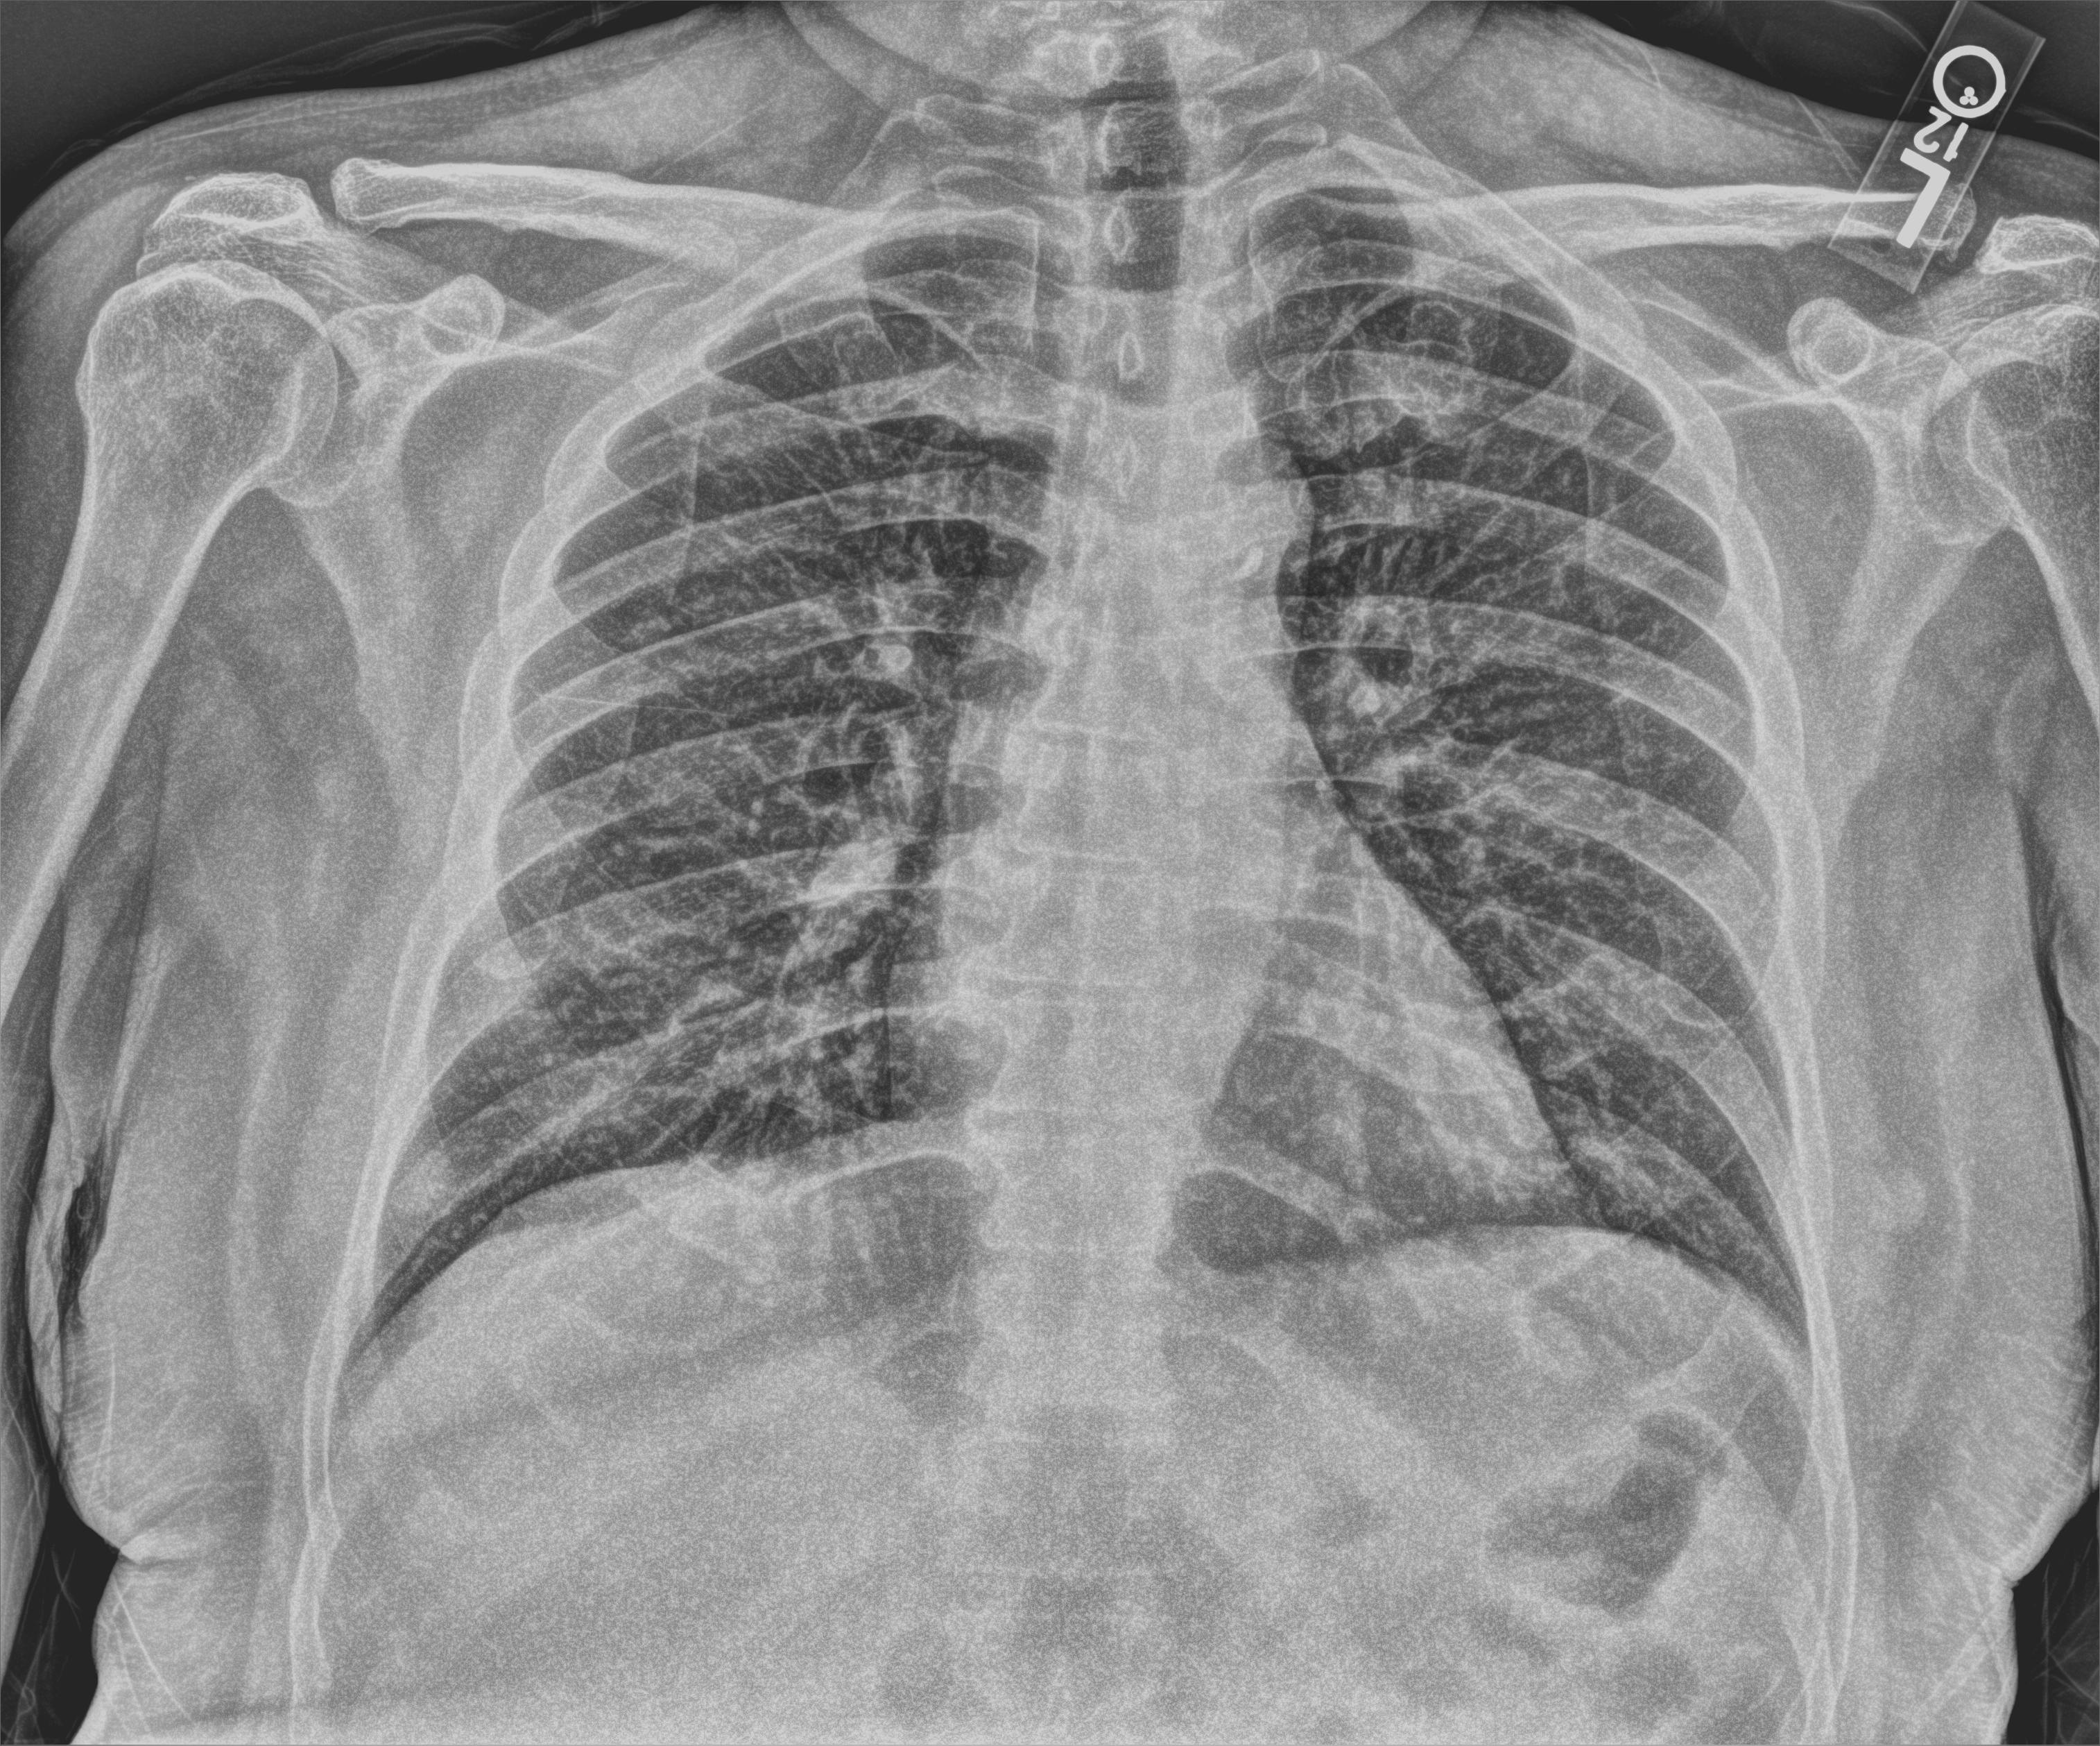
Bedside chest radiograph (computed radiography); anteroposterior (AP) projection. Male patient hospitalised with COVID-19, age 60–74 years.
Admission-level facts for this patient (not findings on this image; timing relative to this image not recorded): mechanically ventilated during this hospital stay: no; length of hospital stay: 1 day.